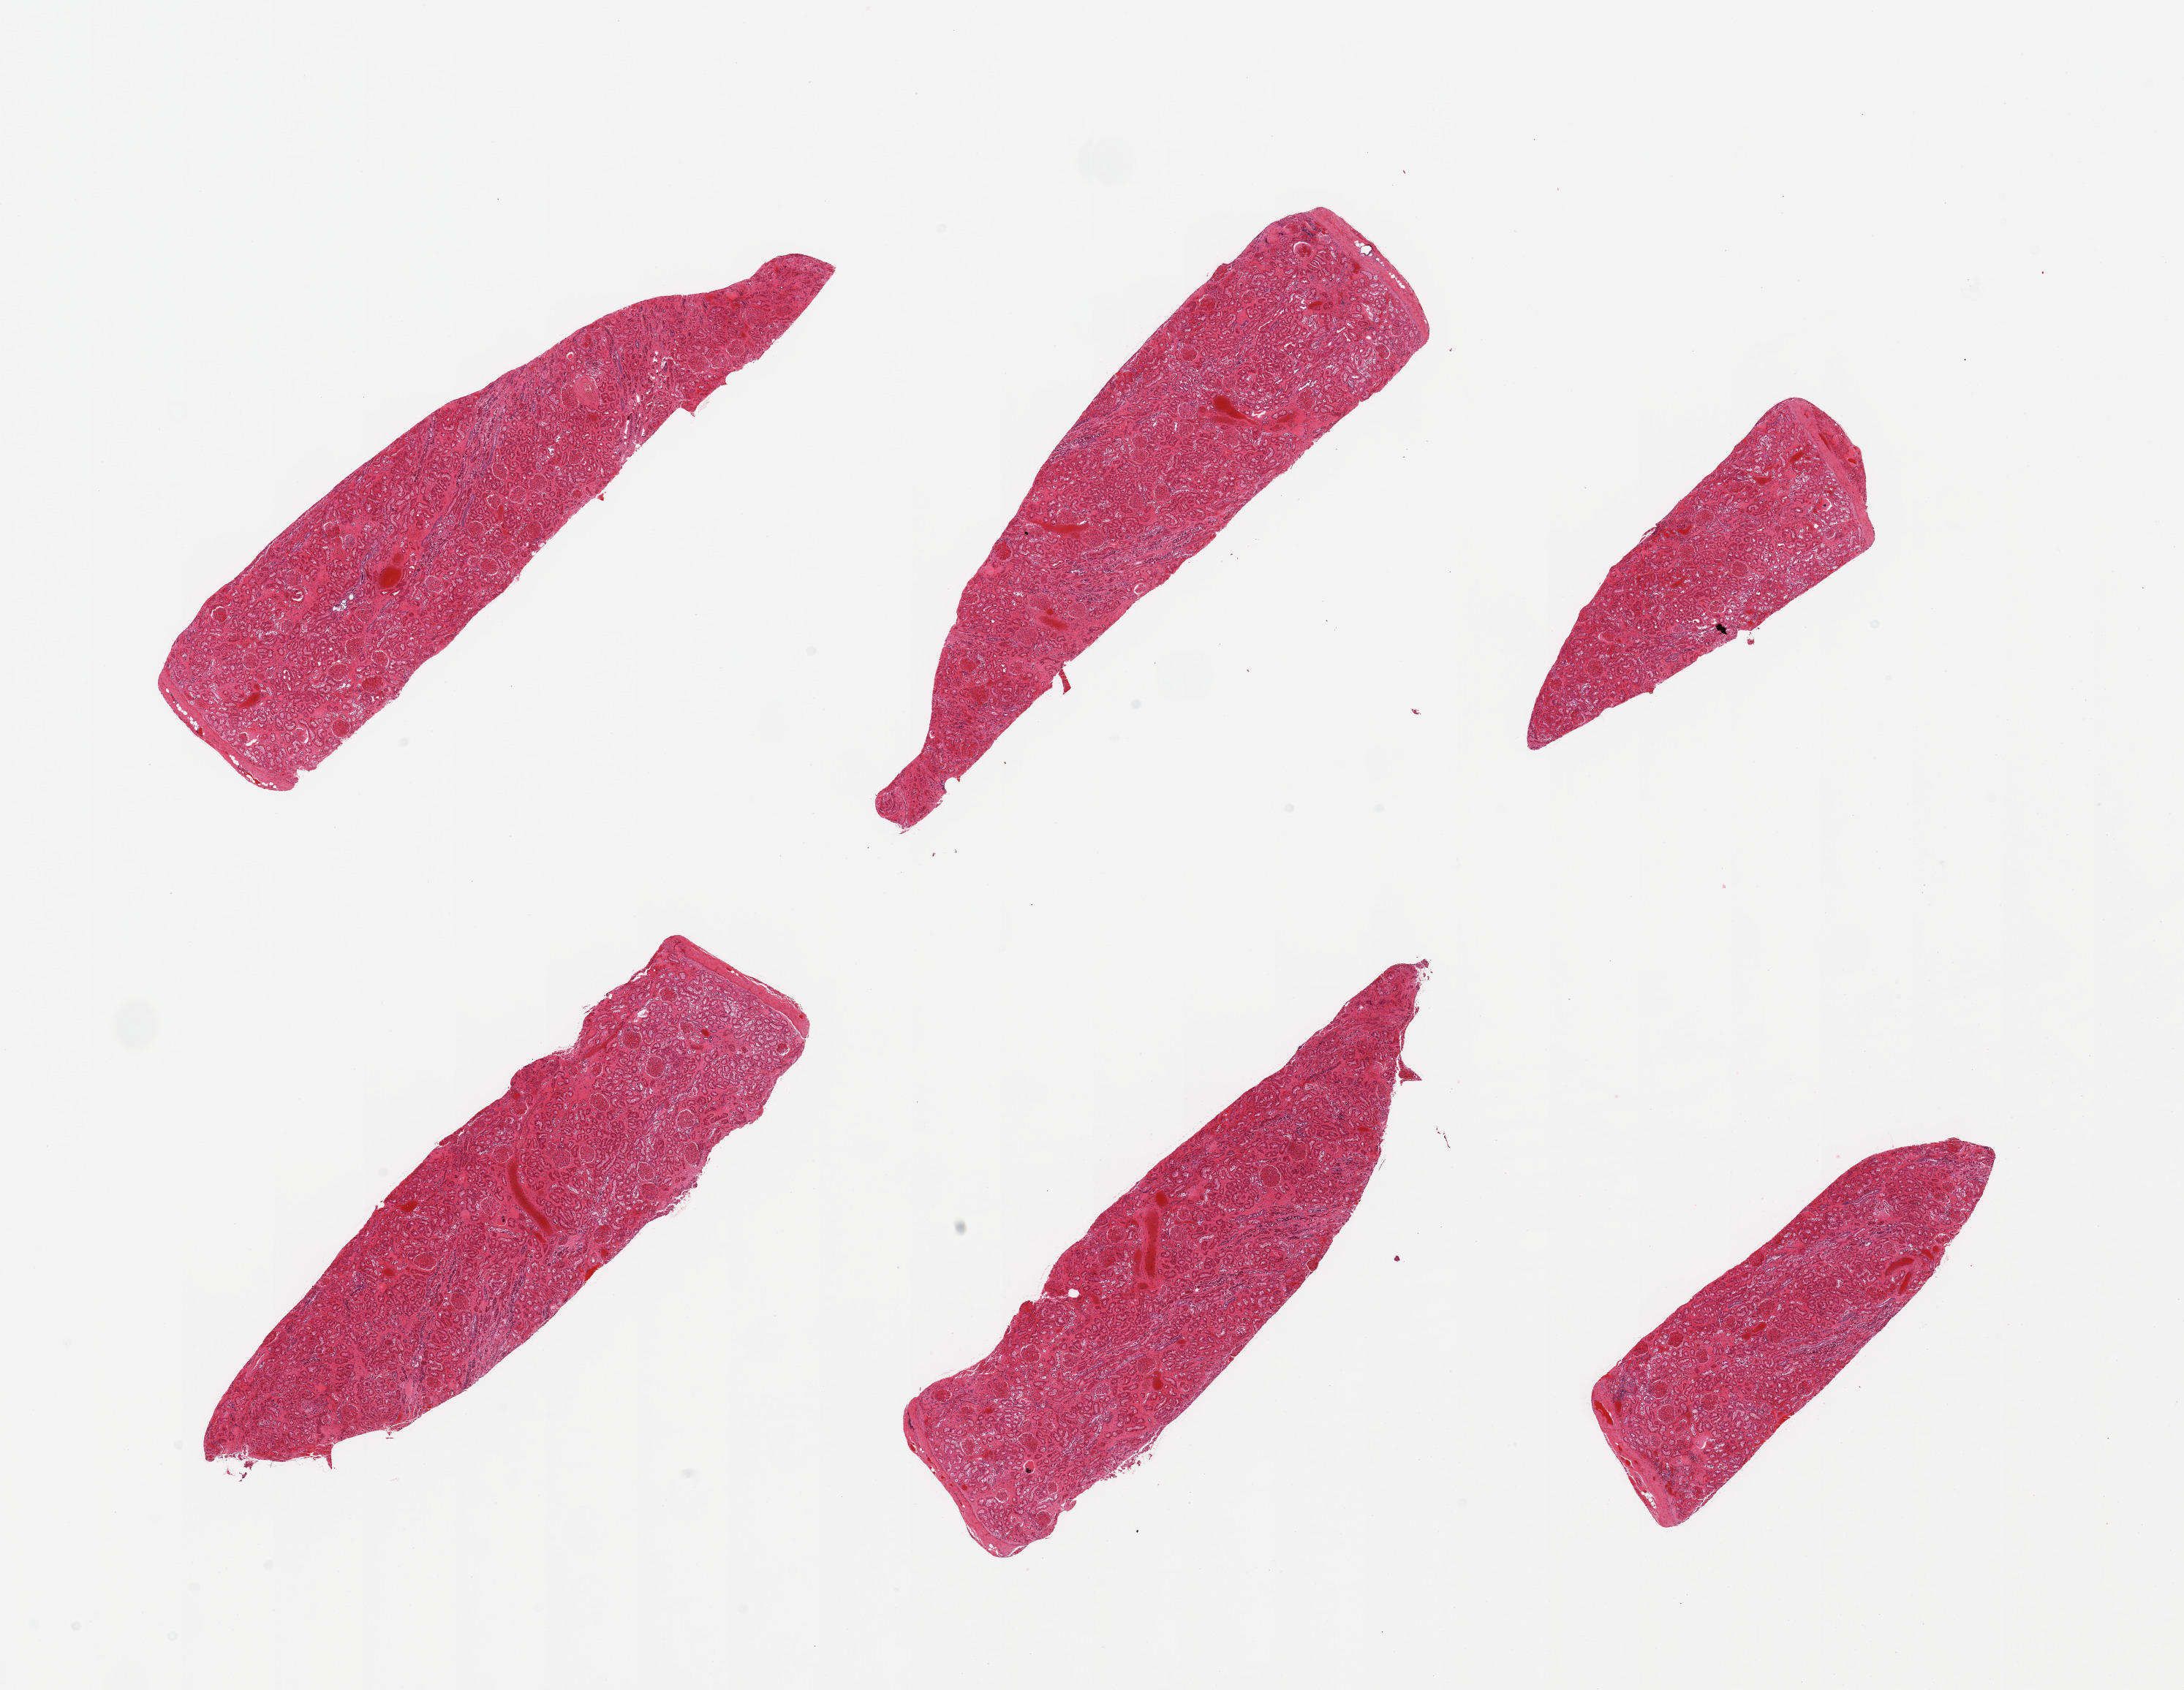
Digitized haematoxylin and eosin-stained section, shown as a low-resolution overview of the whole scanned area (about 23.6 x 18.3 mm, from a 20x scan), PAXgene-fixed, paraffin-embedded tissue, sampled site (target tissue): renal cortex, donor tissue sample. Male donor.
Reviewer comment on this tissue sample: 6 pieces; glomeruli in all sections, congestion, interstitial fibrosis and vascular thickening.